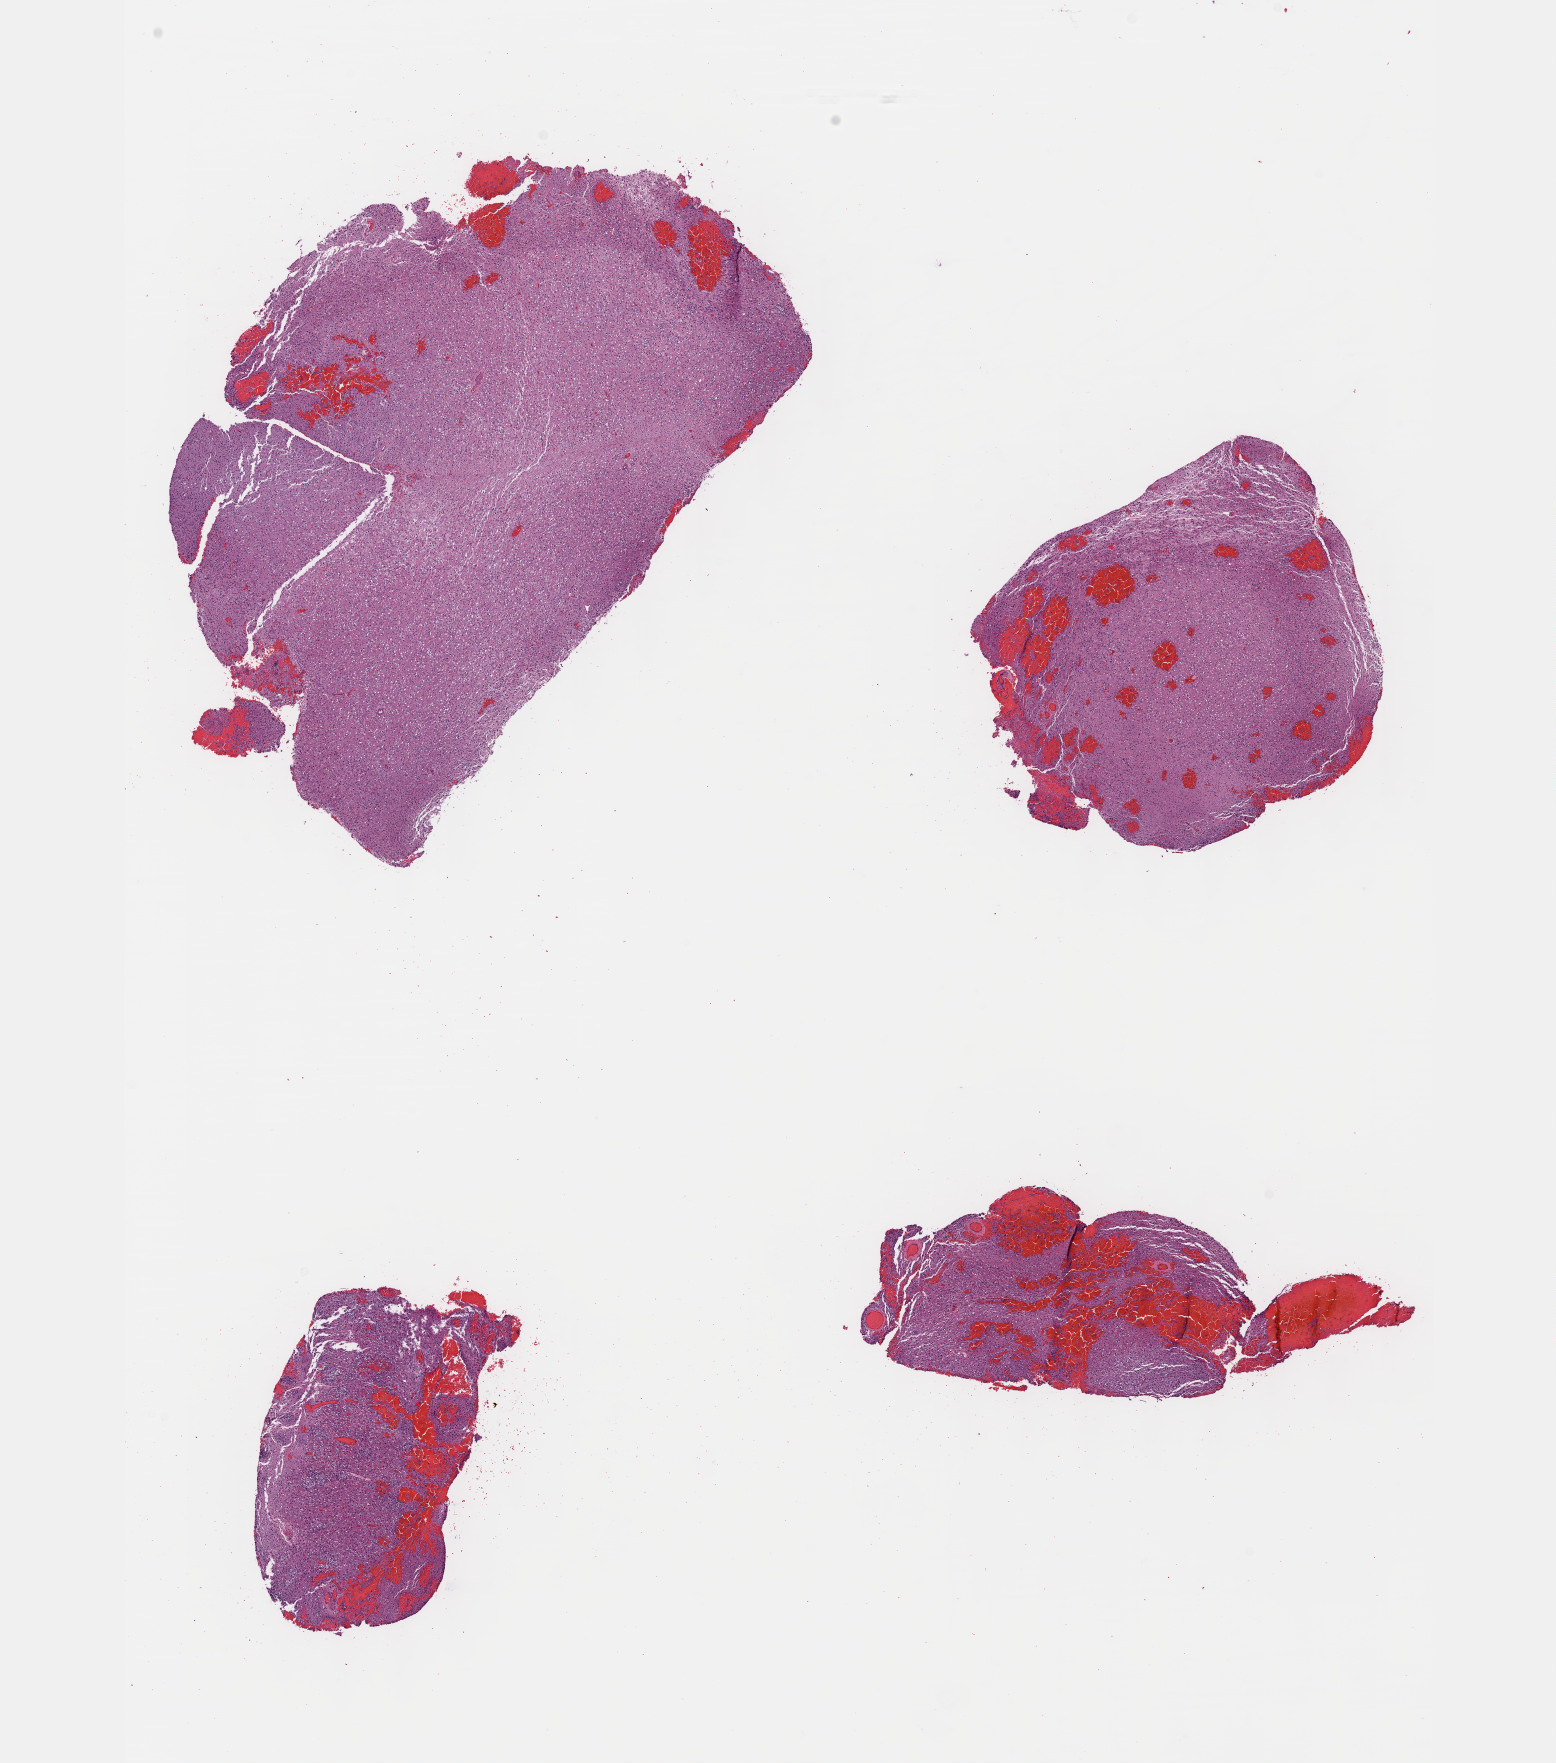
Whole-slide histology image, H&E — a low-resolution overview of the entire scanned area, about 12.6 x 14.2 mm (from a 40x scan); formalin-fixed paraffin-embedded (FFPE) diagnostic section; primary tumour sample from the brain. Male, age 31 years at initial diagnosis.
Diagnosis: Mixed glioma (cerebrum).